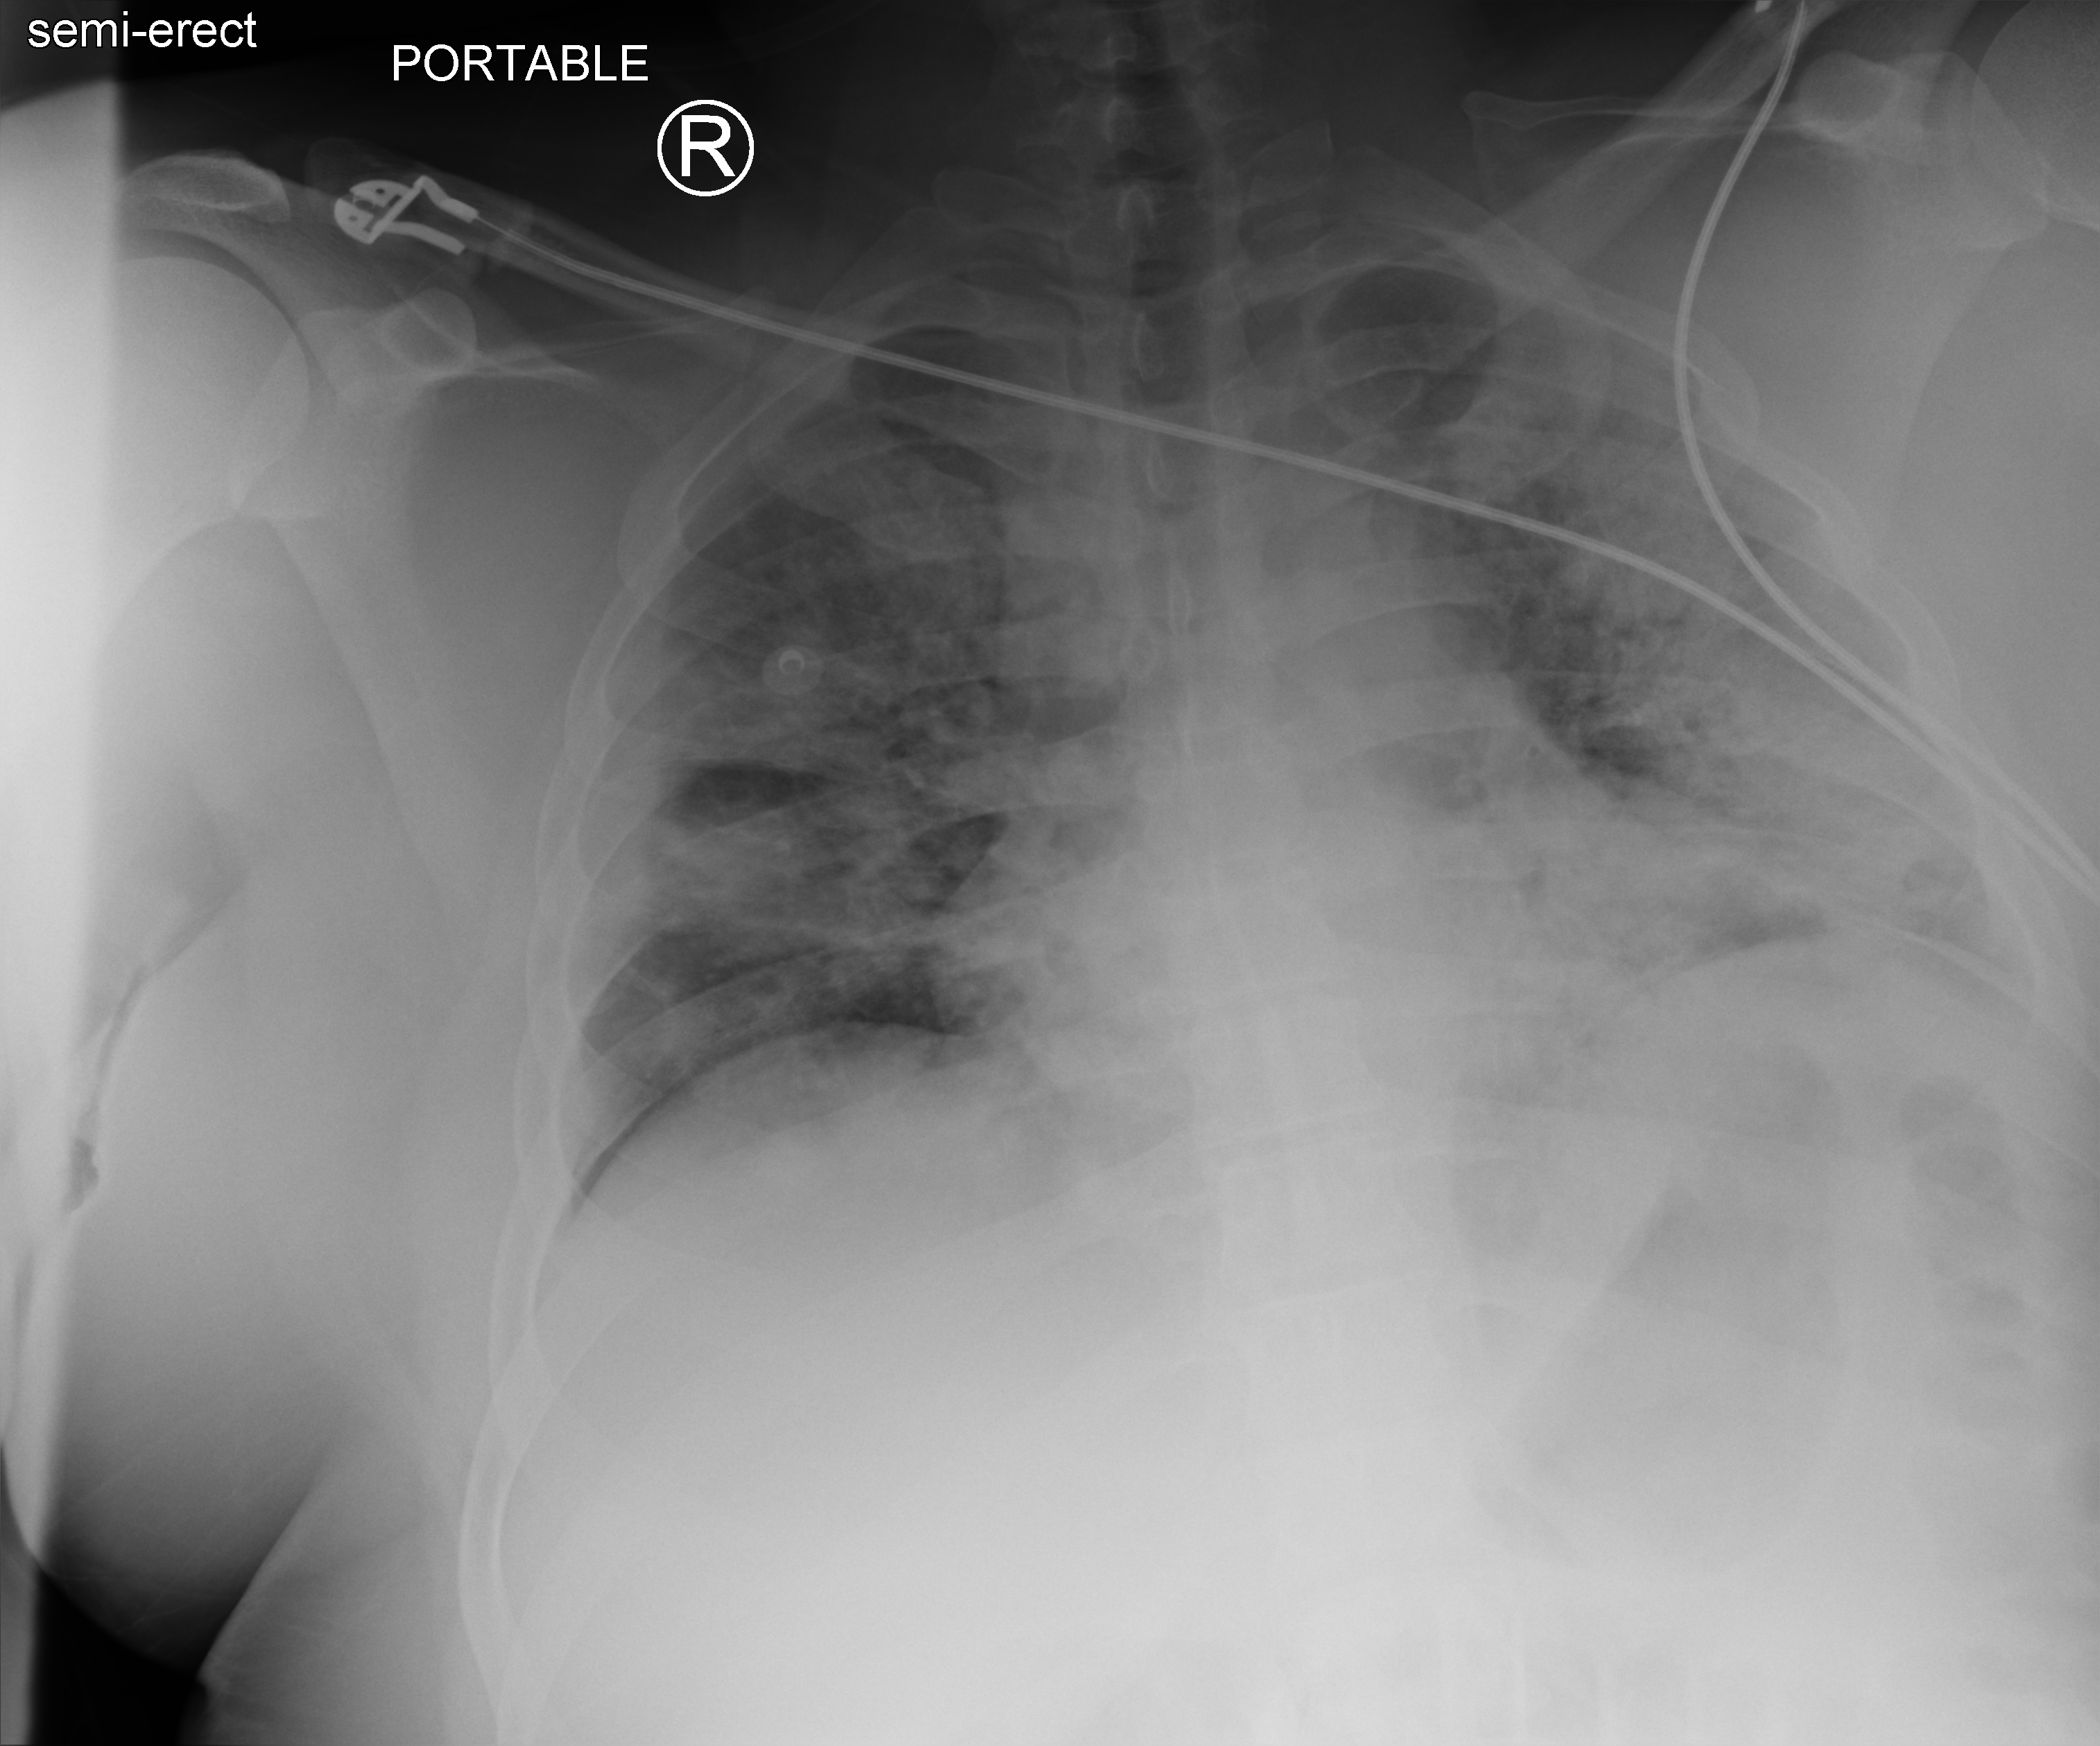
Chest X-ray (portable), anteroposterior (AP) projection. Adult patient hospitalised with COVID-19, age 18–59 years.
Hospital-stay facts (about this admission, not read from this image; timing relative to this image not recorded): admitted to intensive care during this hospital stay: yes; mechanically ventilated during this hospital stay: yes.